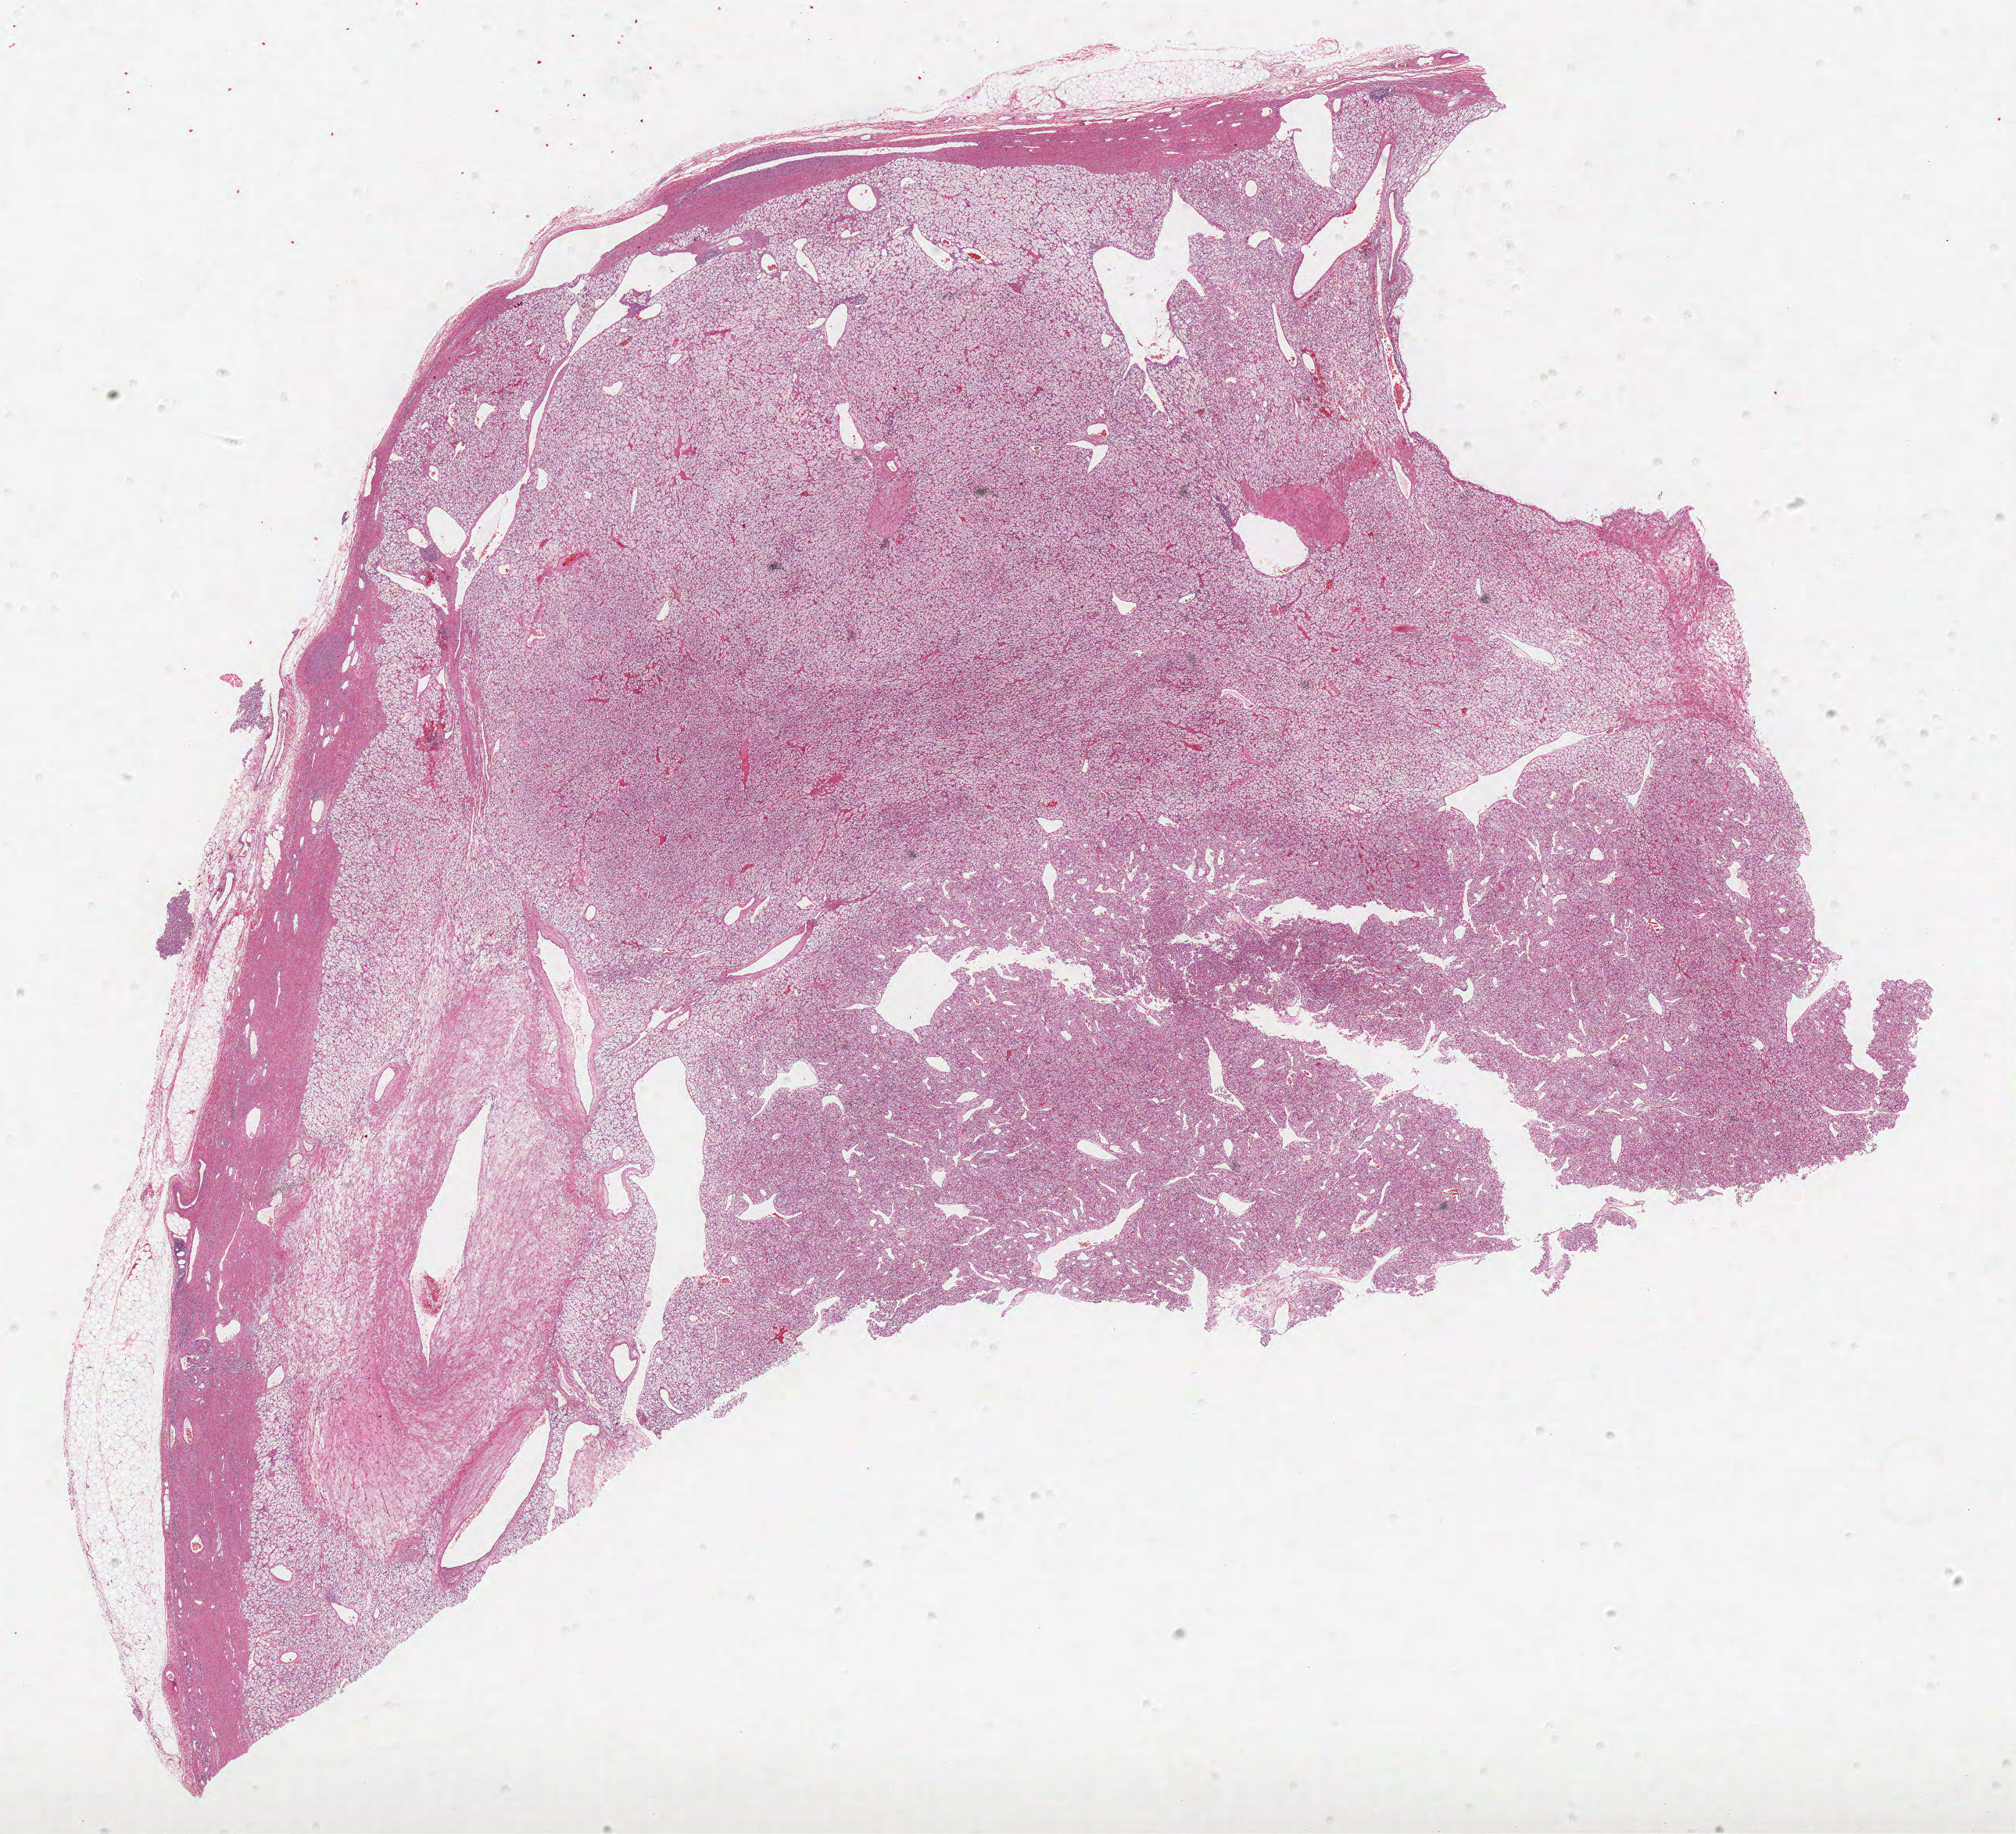
Hematoxylin and eosin (H&E) stained whole-slide image — a low-resolution overview of the entire scanned area, about 20.6 x 18.8 mm, formalin-fixed paraffin-embedded (FFPE) diagnostic section, primary tumour sample from the kidney. Female, age 43 years at initial diagnosis. Histologic grade: G2 (moderately differentiated).
Diagnosis: Clear cell adenocarcinoma, NOS. AJCC pathologic stage: I. TNM: T1b NX M0.